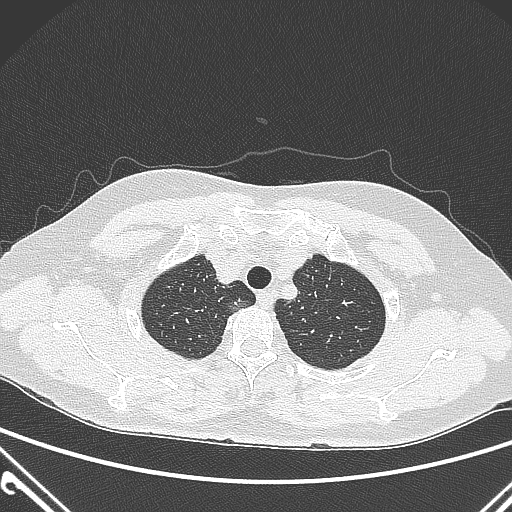
Chest CT, one axial slice; position 245 of 300 along the scan axis; 120 kVp; lung window (W 1500 / L -600 HU); 512 × 512 image matrix. Patient: female, 54 years. From the clinical record (not read from this slice): clinical TNM (as recorded): T1a N0 M0.
Annotated regions visible in this slice (rectangle marked by the reading radiologist):
- lung tumour (recorded histology: adenocarcinoma): bounding box [x1, y1, x2, y2] px = [223, 297, 253, 318]